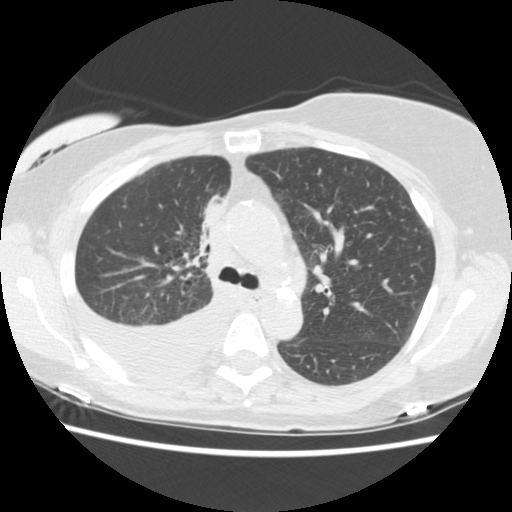
Low-dose screening chest CT, one axial slice. Slice 101 of 157 in the series (ordered by position). Reconstruction kernel STANDARD. Lung window (W 1500 / L -600 HU). 2.5 mm slice thickness. 512 × 512 image matrix.
Outlined on this slice (manually delineated by an expert):
- lesion 1 (tumor, upper lobe of right lung): bounding box [x1, y1, x2, y2] px = [202, 201, 225, 228]